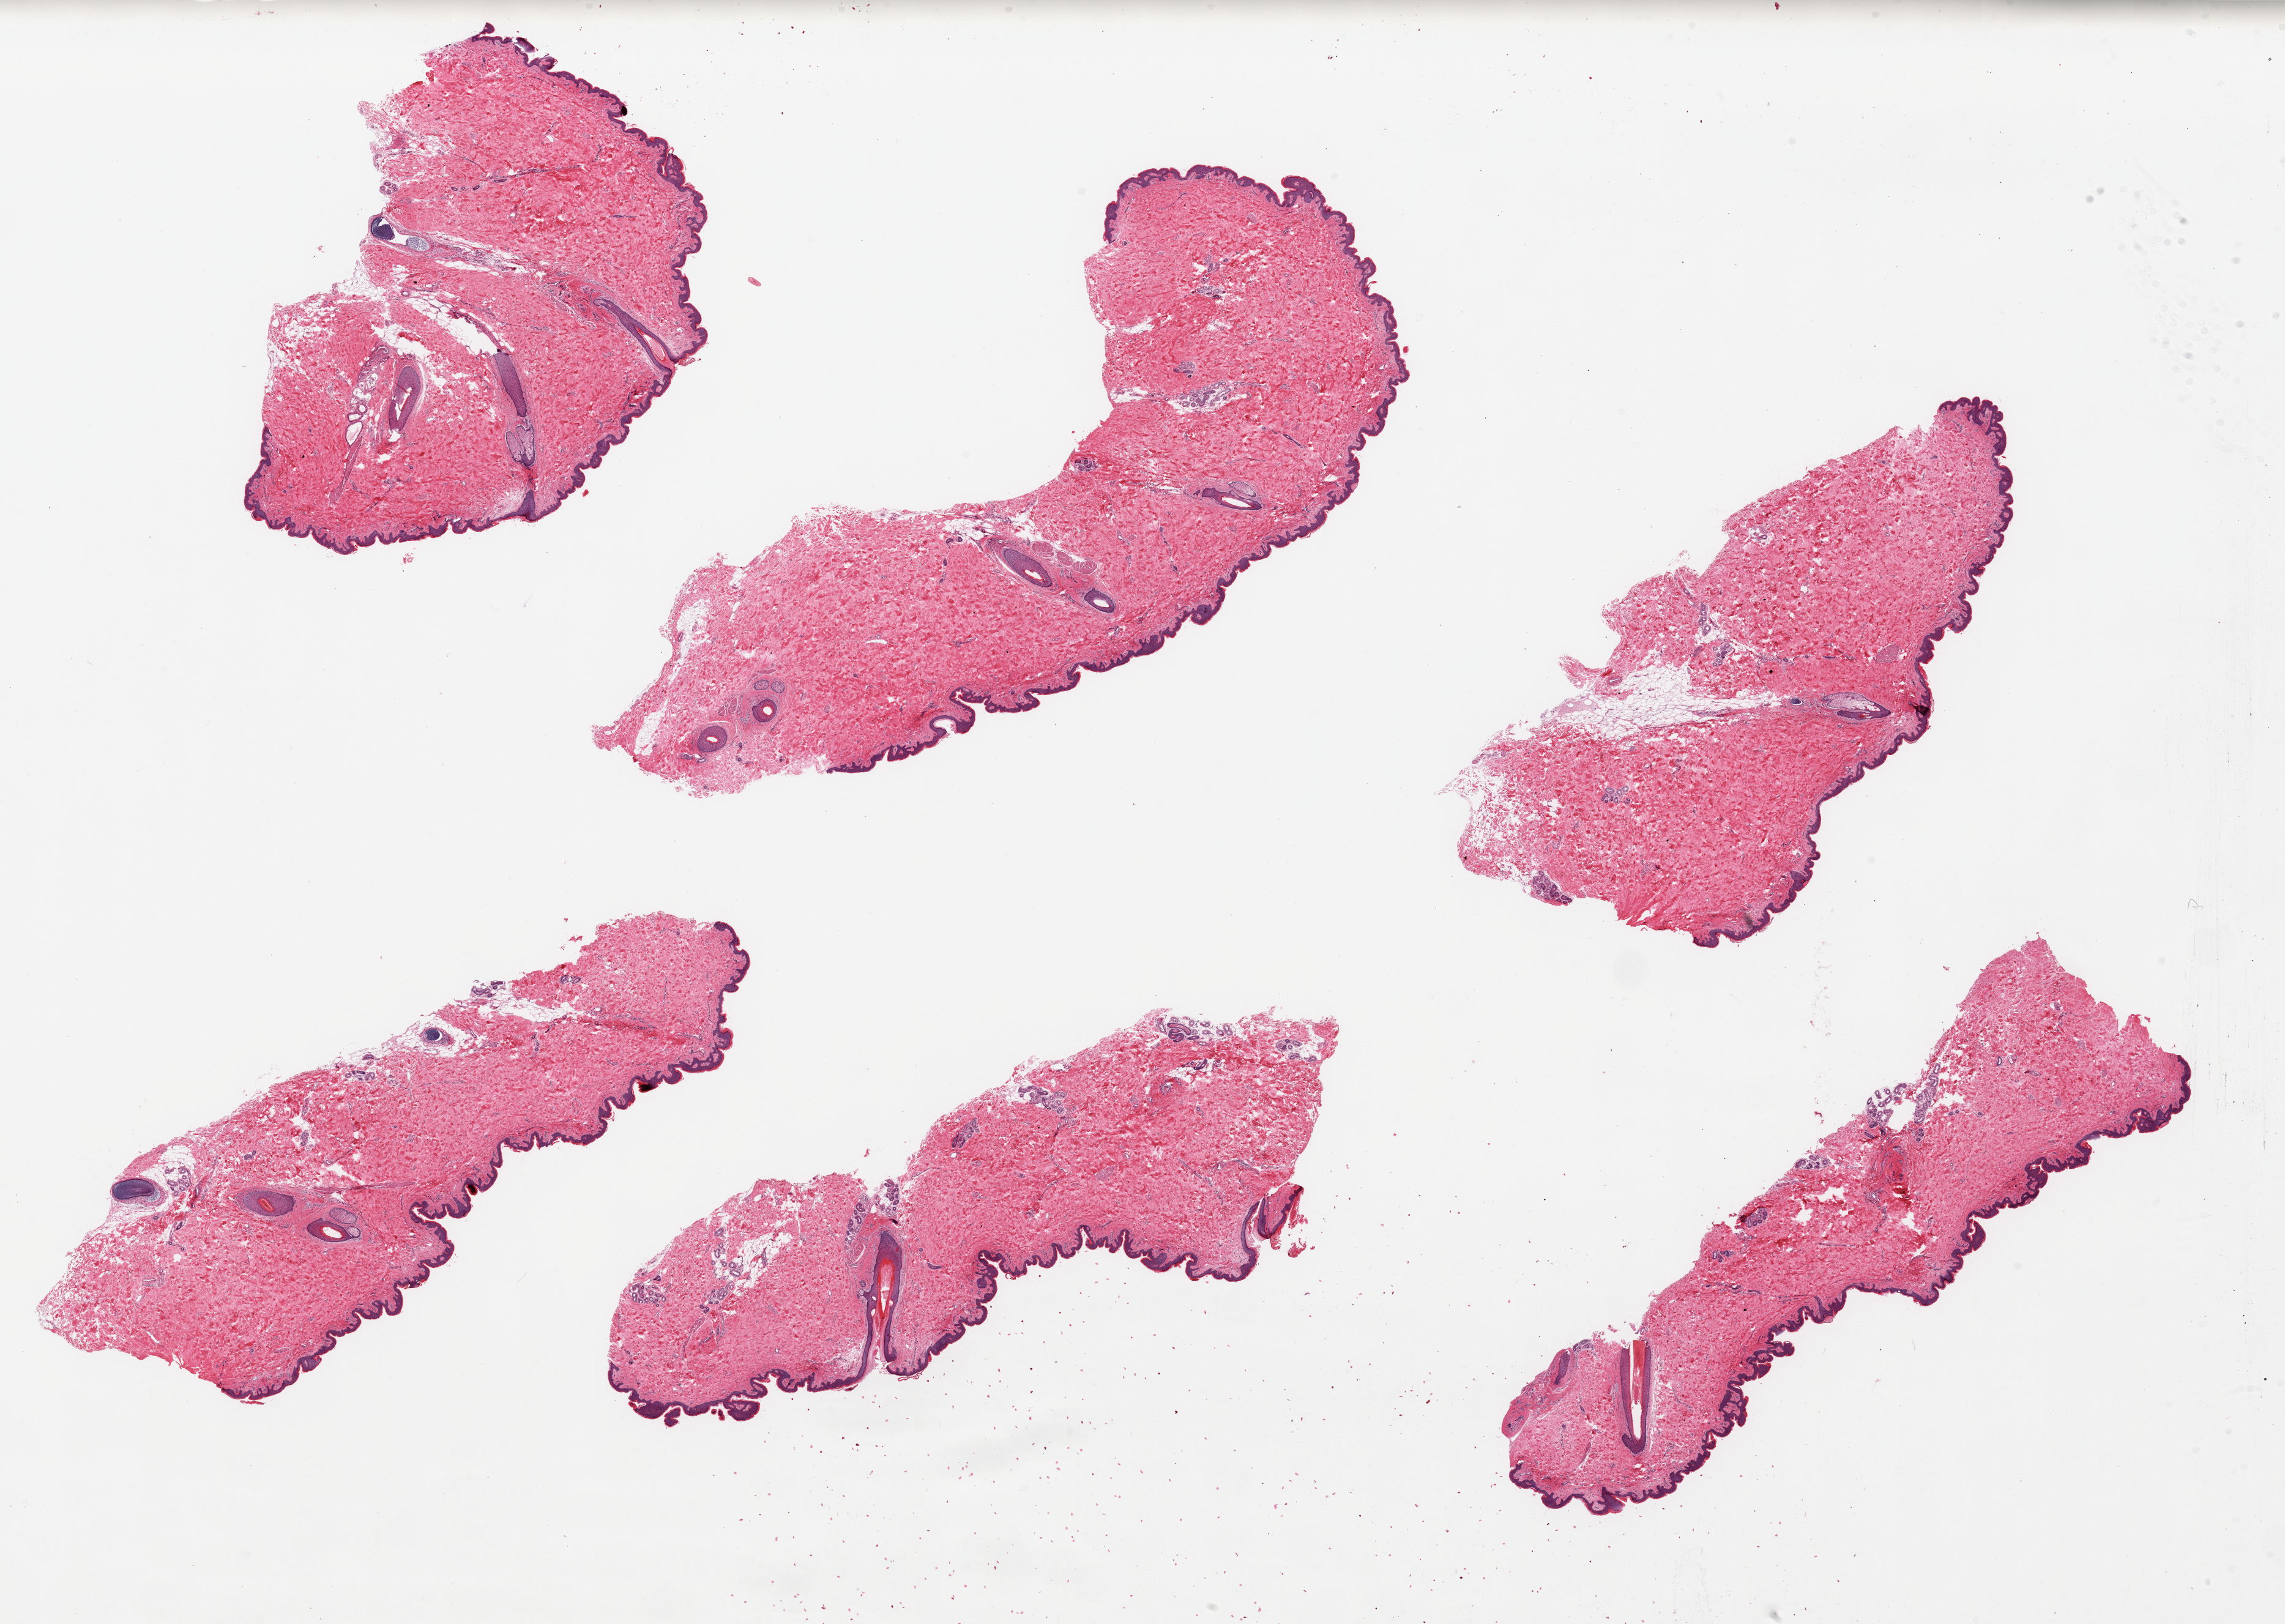
Digitized H&E-stained section, whole scanned area (about 29.5 x 21.0 mm, acquisition: 20x scan) shown as a low-resolution overview. PAXgene-fixed paraffin-embedded (PFPE) section. Section of skin of suprapubic region (target tissue). Tissue donor sample. Donor: male.
* reviewer comment on this tissue sample: 6 pieces; well trimmed, up to 10% internal fat, hair-bearing skin